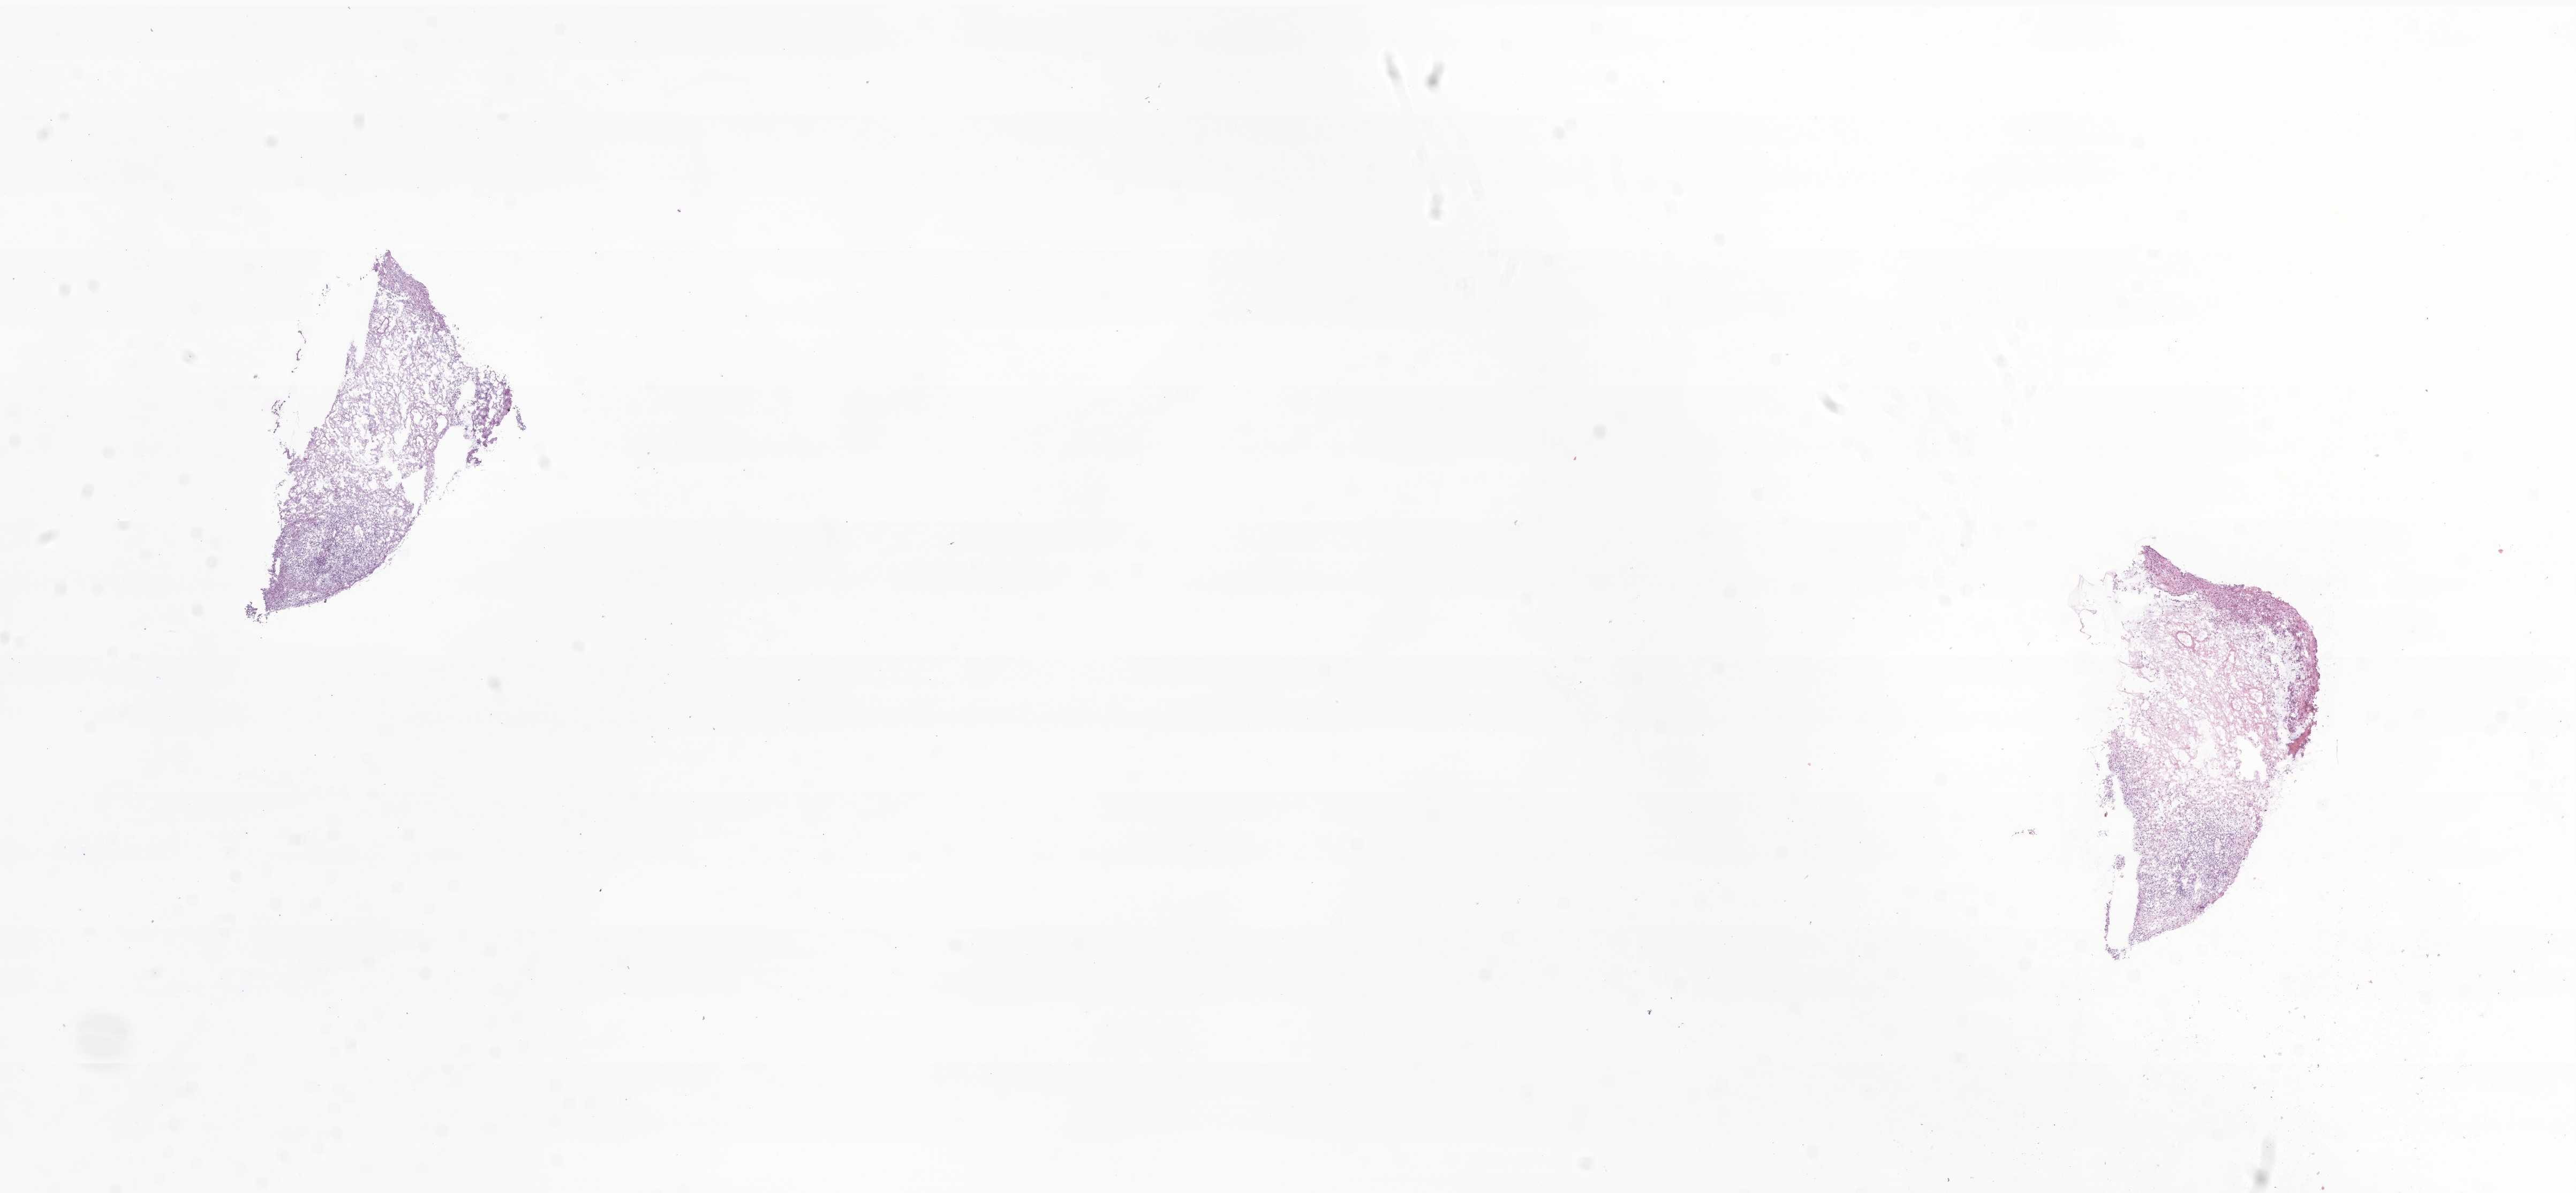
Haematoxylin and eosin whole-slide image of tumor tissue from the cerebrum — low-resolution overview of the scanned area, about 20.3 x 9.4 mm. Cryosection (OCT / tissue freezing medium). Patient: female, age 374 days (about 1.0 years).
Recorded diagnosis: Ganglioglioma, NOS.